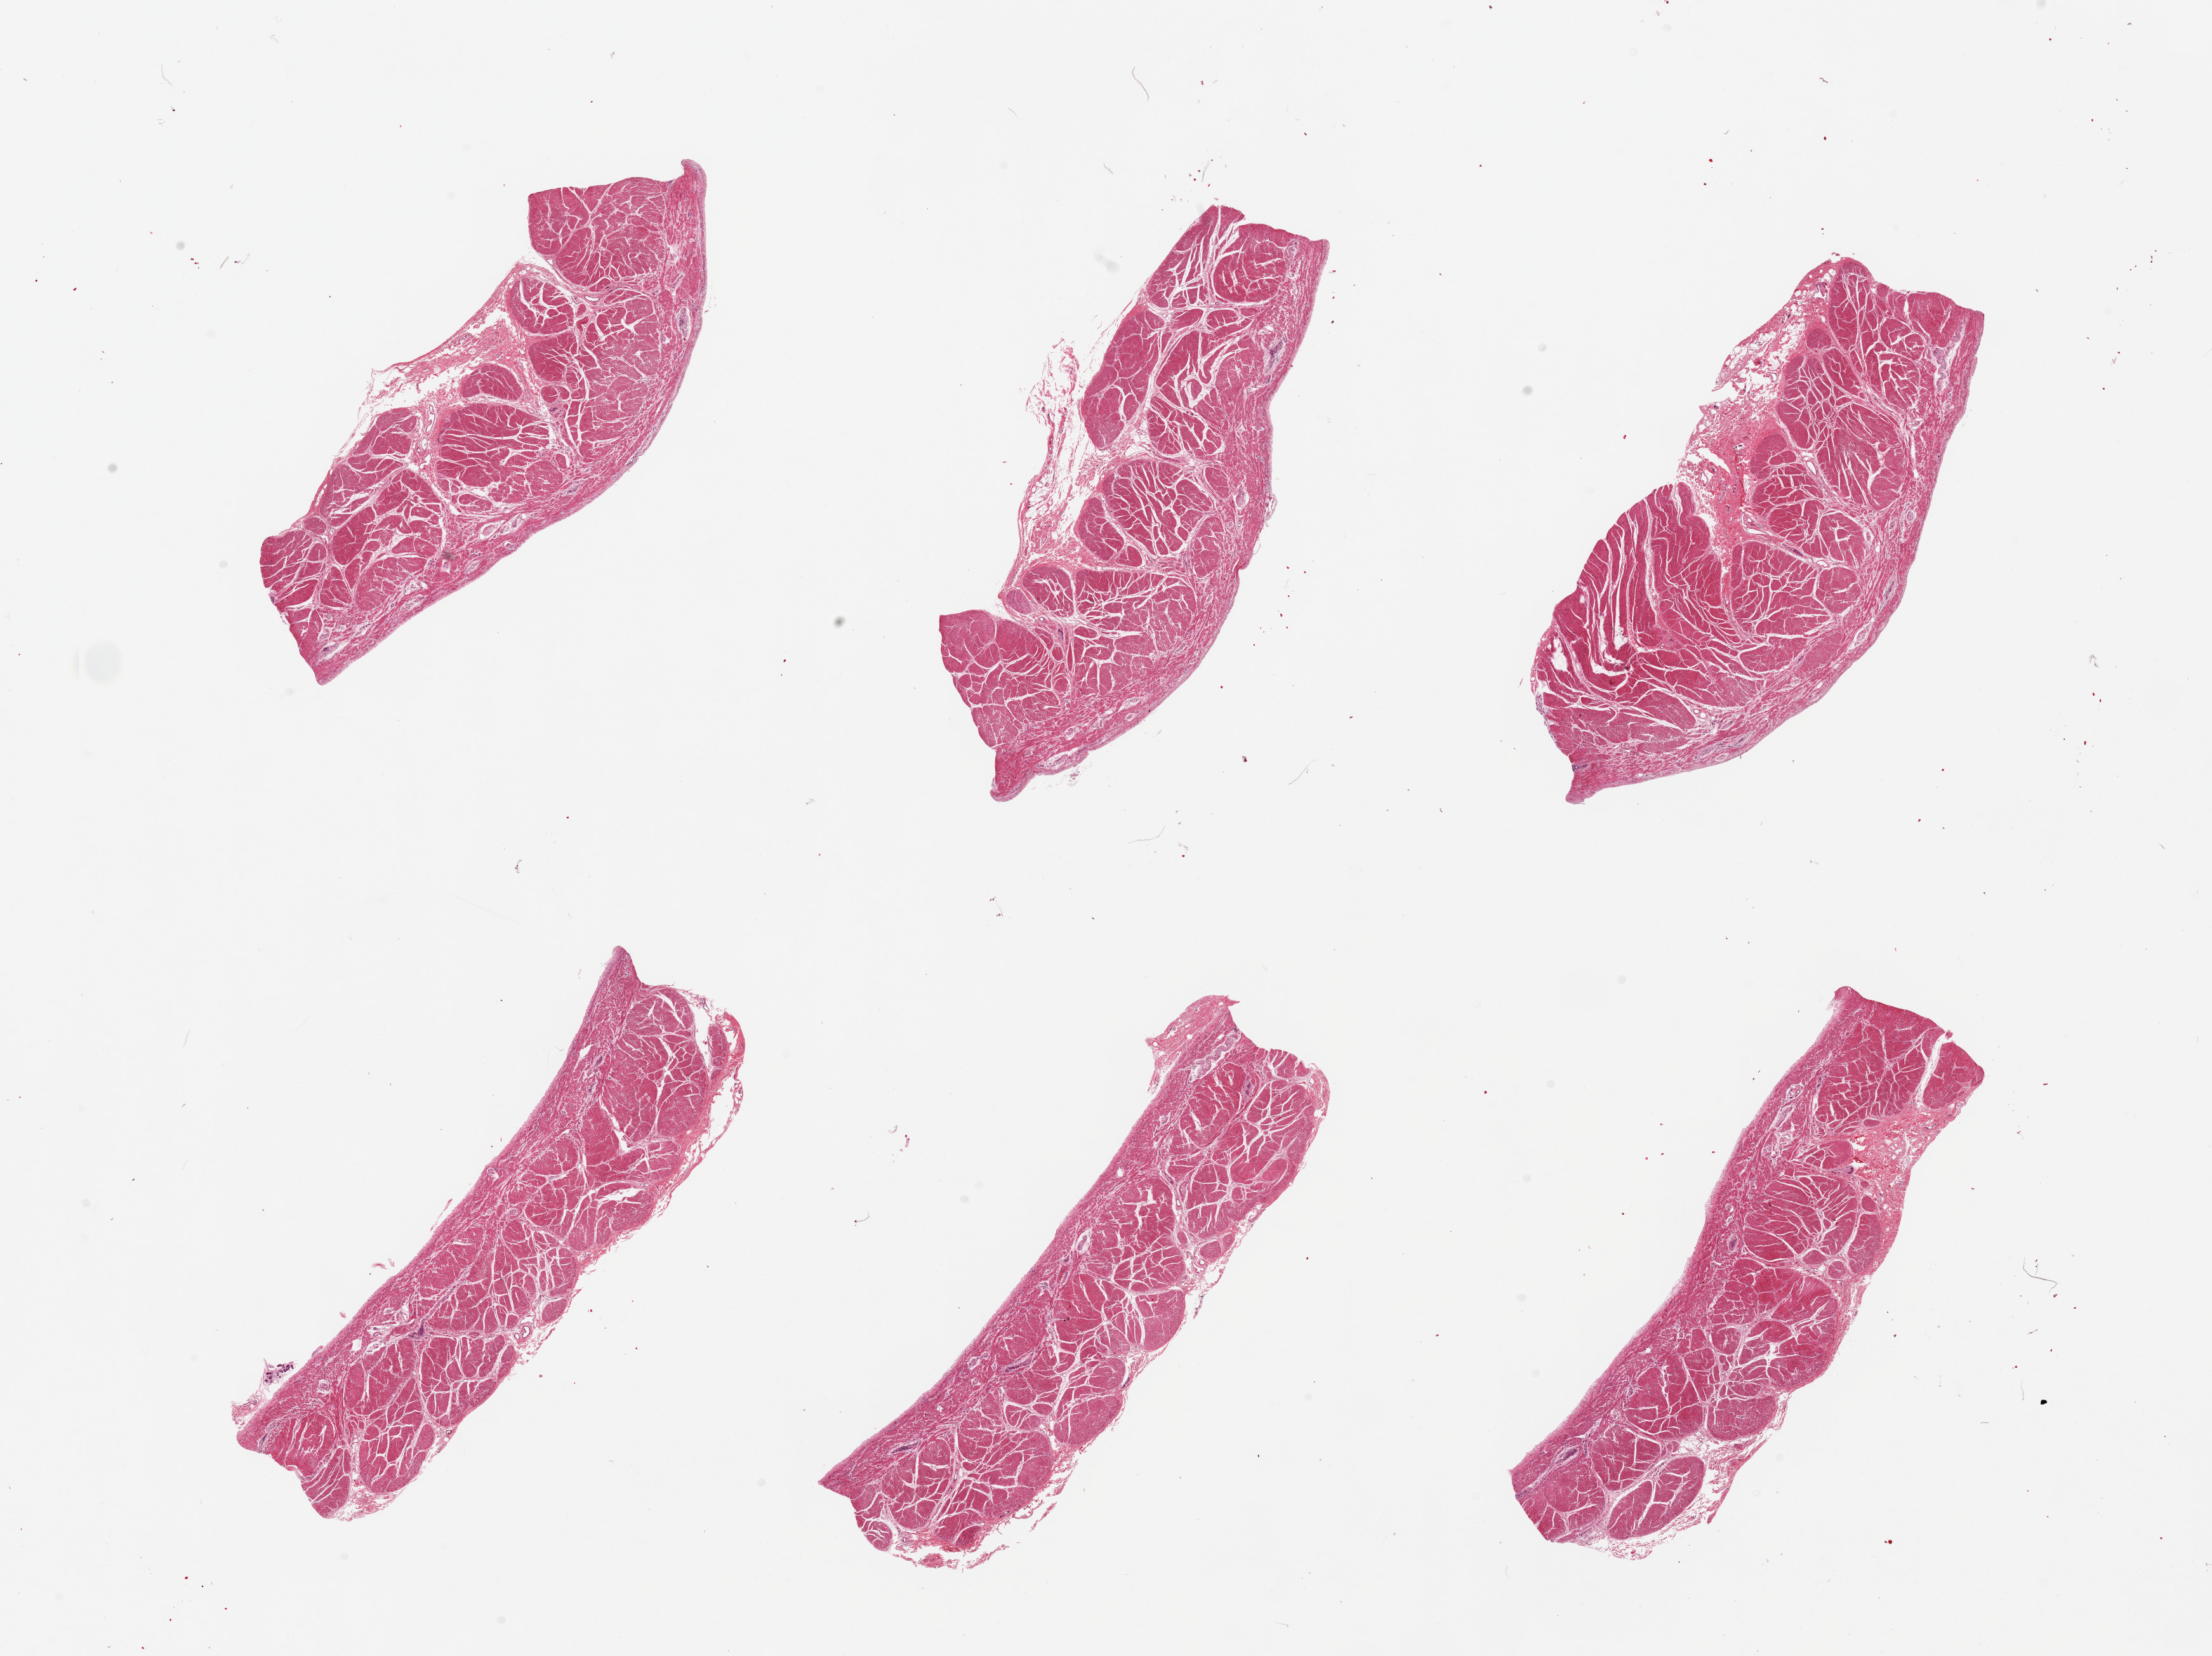
Digitized H&E-stained section, brightfield, whole scanned area (about 27.6 x 20.6 mm) shown as a low-resolution overview, PAXgene-fixed paraffin-embedded (PFPE) section, section of stomach (target tissue), donor tissue sample. Female donor.
• review note (as recorded): 6 pieces, mucosa totoally denuded/sloughed, muscularis only